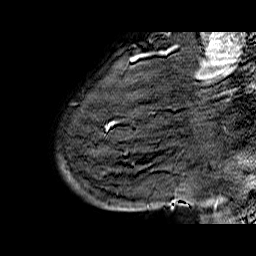
Breast MRI (dynamic contrast-enhanced), one sagittal slice; dynamic contrast-enhanced series, time point 2 of 6 at this slice position (early post-contrast); 1.5 T; TE 6.5 ms, TR 32.9 ms; 256 × 256 image matrix, field of view 200 × 200 mm. Female patient. Case-level facts recorded for this patient, not image findings: setting: breast cancer imaged before/during neoadjuvant chemotherapy; receptor status: HR-positive, HER2-negative.
Outlined on this slice (semi-automatic segmentation, software-assisted and operator-edited):
- analysis volume of interest (the breast-tissue region the enhancement analysis was run in; not a lesion): box from (x=58, y=74) to (x=176, y=210) px
- tumour enhancement mask (voxels above the 100 % enhancement threshold inside the analysis volume of interest): (x=170, y=202)–(x=172, y=204)